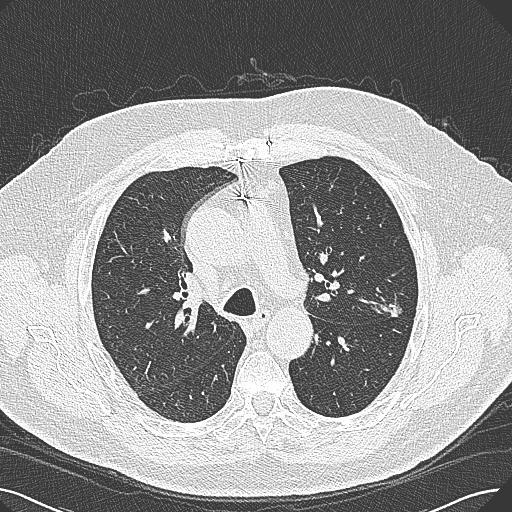
Axial slice from a low-dose chest CT screening exam; baseline annual screen; lung window (W 1500 / L -600 HU); 512 × 512 image matrix, field of view 370 × 370 mm. Male, age 74 years at enrolment.
Expert reader's lesion annotation, box from (x=365, y=274) to (x=428, y=327) px. Reader record for this screening exam (exam-level; its link to the box is not recorded): non-calcified nodule or mass ≥4 mm, left upper lobe, 15 × 10 mm, poorly defined margins, soft tissue attenuation. Official screen result: positive, change unspecified: nodule(s) >= 4 mm or enlarging nodule(s), mass(es), or other non-specific abnormalities suspicious for lung cancer. Participant outcome: lung cancer diagnosed 124 days after this screen — adenocarcinoma, NOS, left upper lobe, well differentiated (G1), stage IA (AJCC 6th edition), 26 mm at pathology.